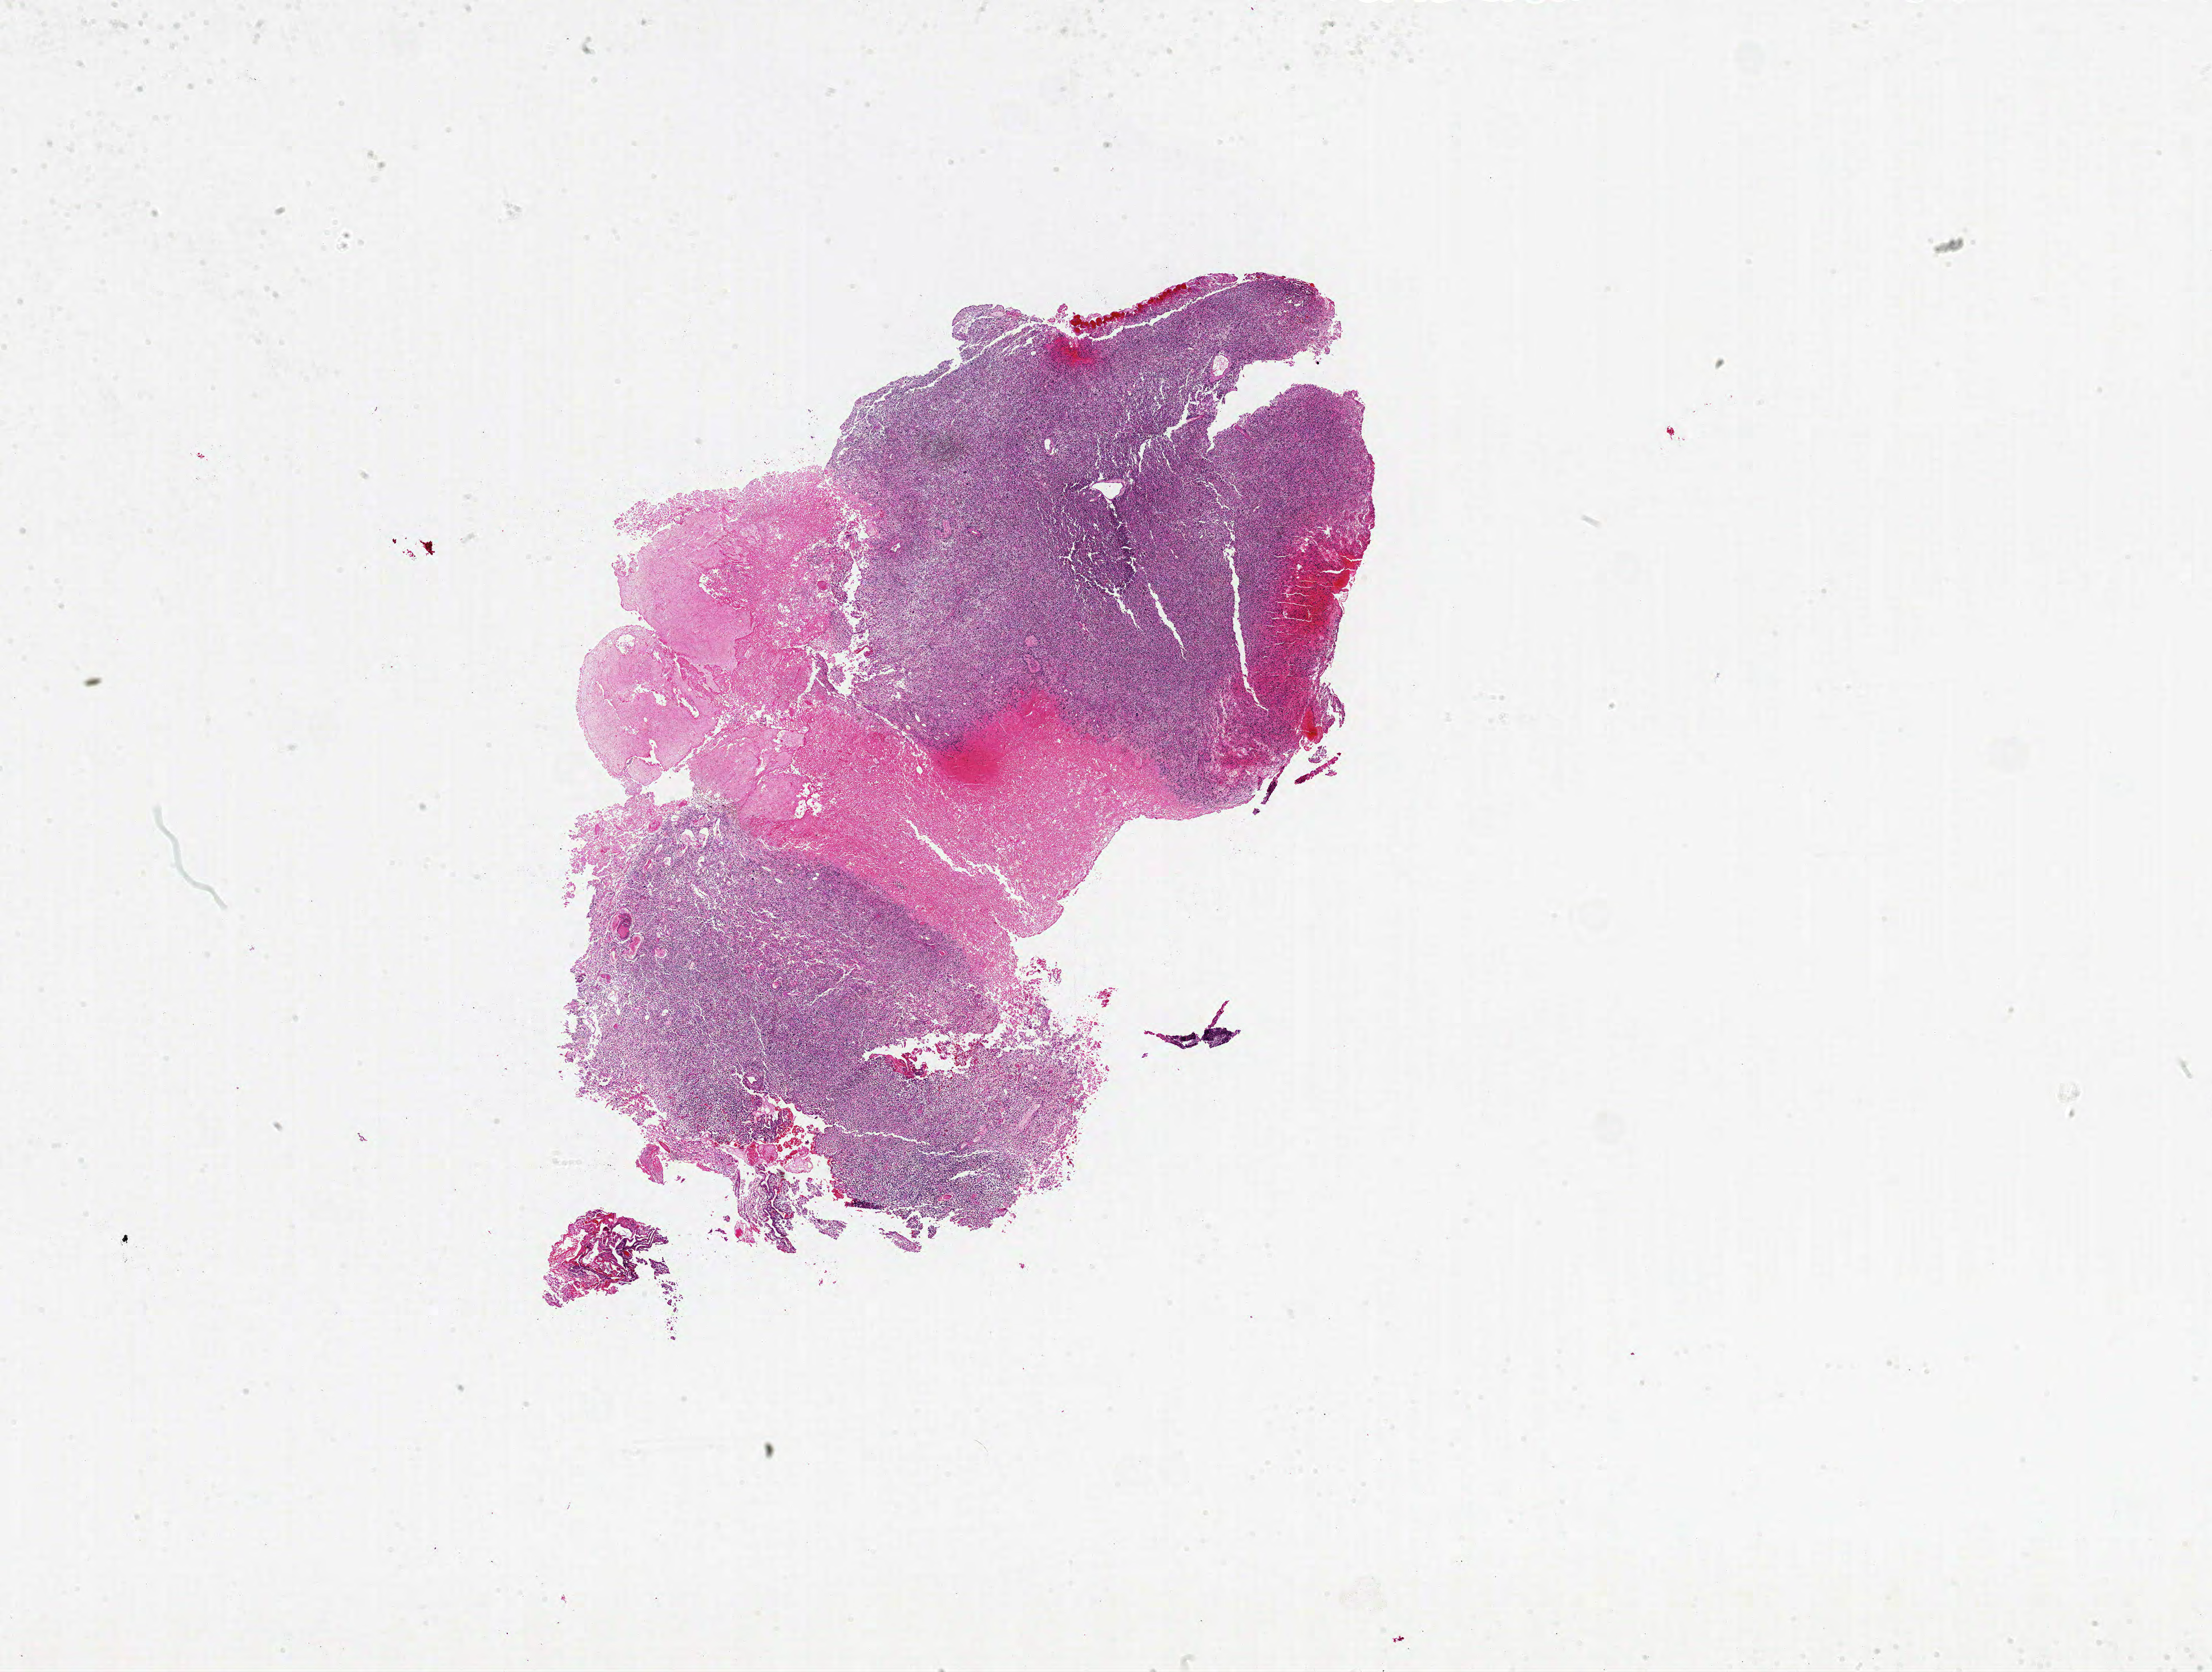
Hematoxylin and eosin (H&E) stained whole-slide image, low-resolution overview of the scanned area, about 31.0 x 23.4 mm; FFPE section; sample: primary tumour, brain. Patient: male, age at initial diagnosis 86 years.
- pathologic diagnosis: Glioblastoma